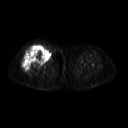
FDG PET of an extremity soft-tissue mass (from a PET/CT study), one axial slice. 3.27 mm slice thickness. 128 × 128 image matrix. Female patient, age 57 years. From the clinical record (not read from this slice): histological type: pleiomorphic undifferentiated sarcoma; grade: high; site of the primary tumour: right quadricep.
Outlined on this slice (expert contour drawn on MRI and transferred to this co-registered scan by the dataset authors):
- tumour plus oedema (research contour): bounding box <22,45,50,73> (left, top, right, bottom; pixels)
- tumour (research contour): <22,45,50,73>